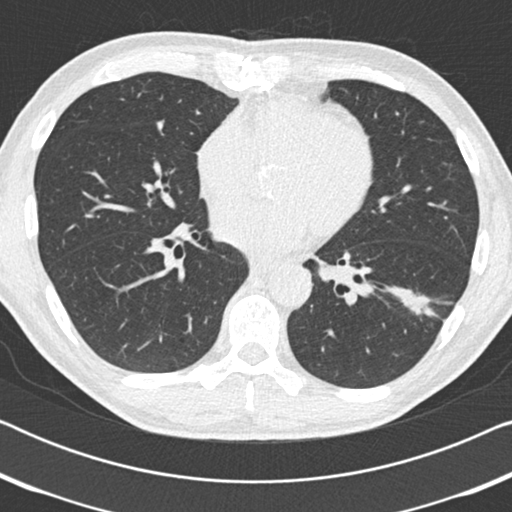
Low-dose screening chest CT, one axial slice. Position 82 of 186 along the scan axis. 120 kVp. Lung window (W 1500 / L -600 HU). 2 mm slice thickness. 512 × 512 image matrix.
Structures marked on this image (expert manual segmentation):
- lesion 1 (tumor, lower lobe of left lung): bounding box (x1, y1, x2, y2) in pixels: (402, 294, 434, 317)